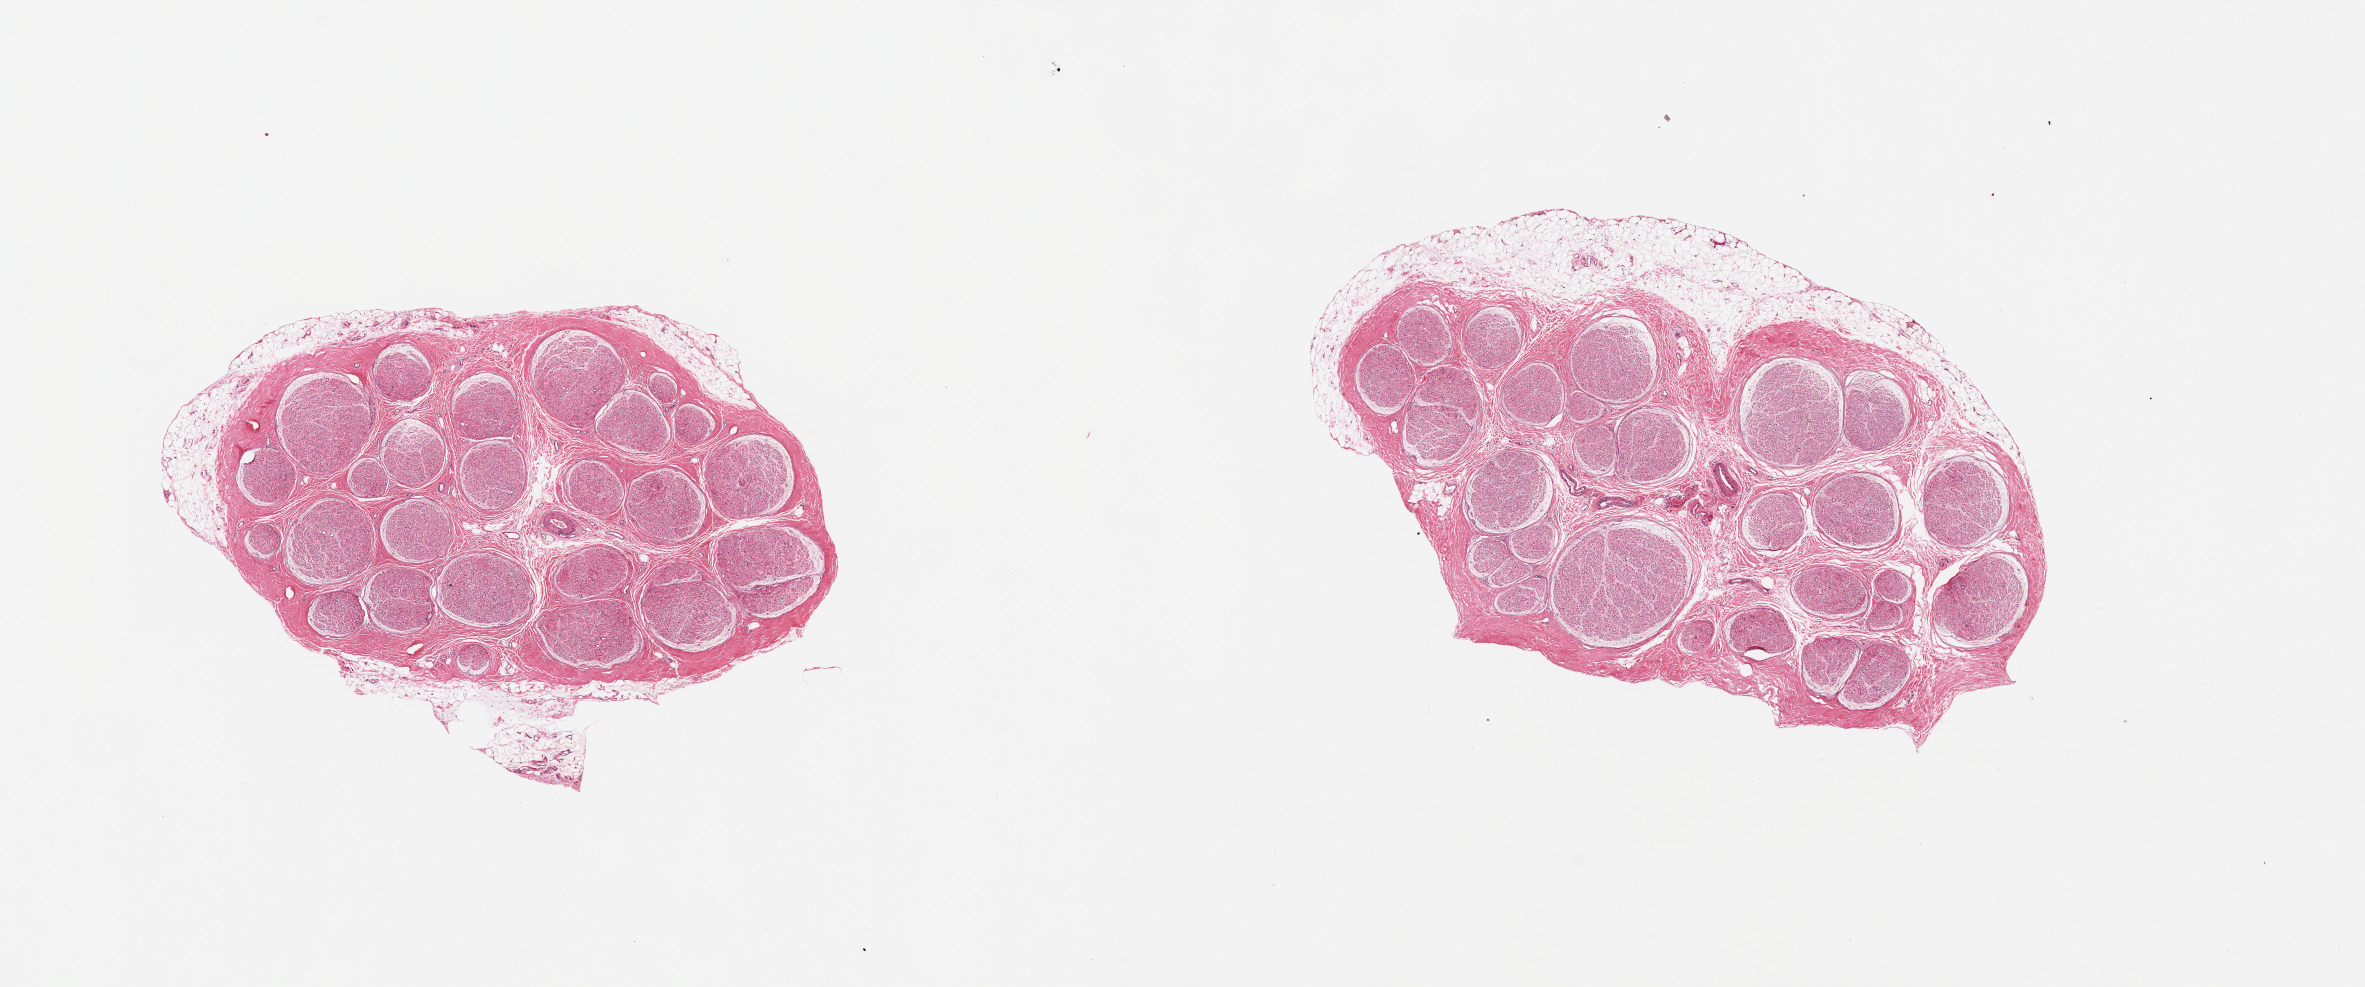
Whole-slide image, haematoxylin and eosin stain, brightfield — whole scanned area (about 18.7 x 7.8 mm) shown as a low-resolution overview; PAXgene-fixed, paraffin-embedded tissue; sampled site (target tissue): tibial nerve; tissue donor sample. Donor sex: male.
Reviewer comment on this tissue sample: 2 pieces; 20 & 10% external fat.